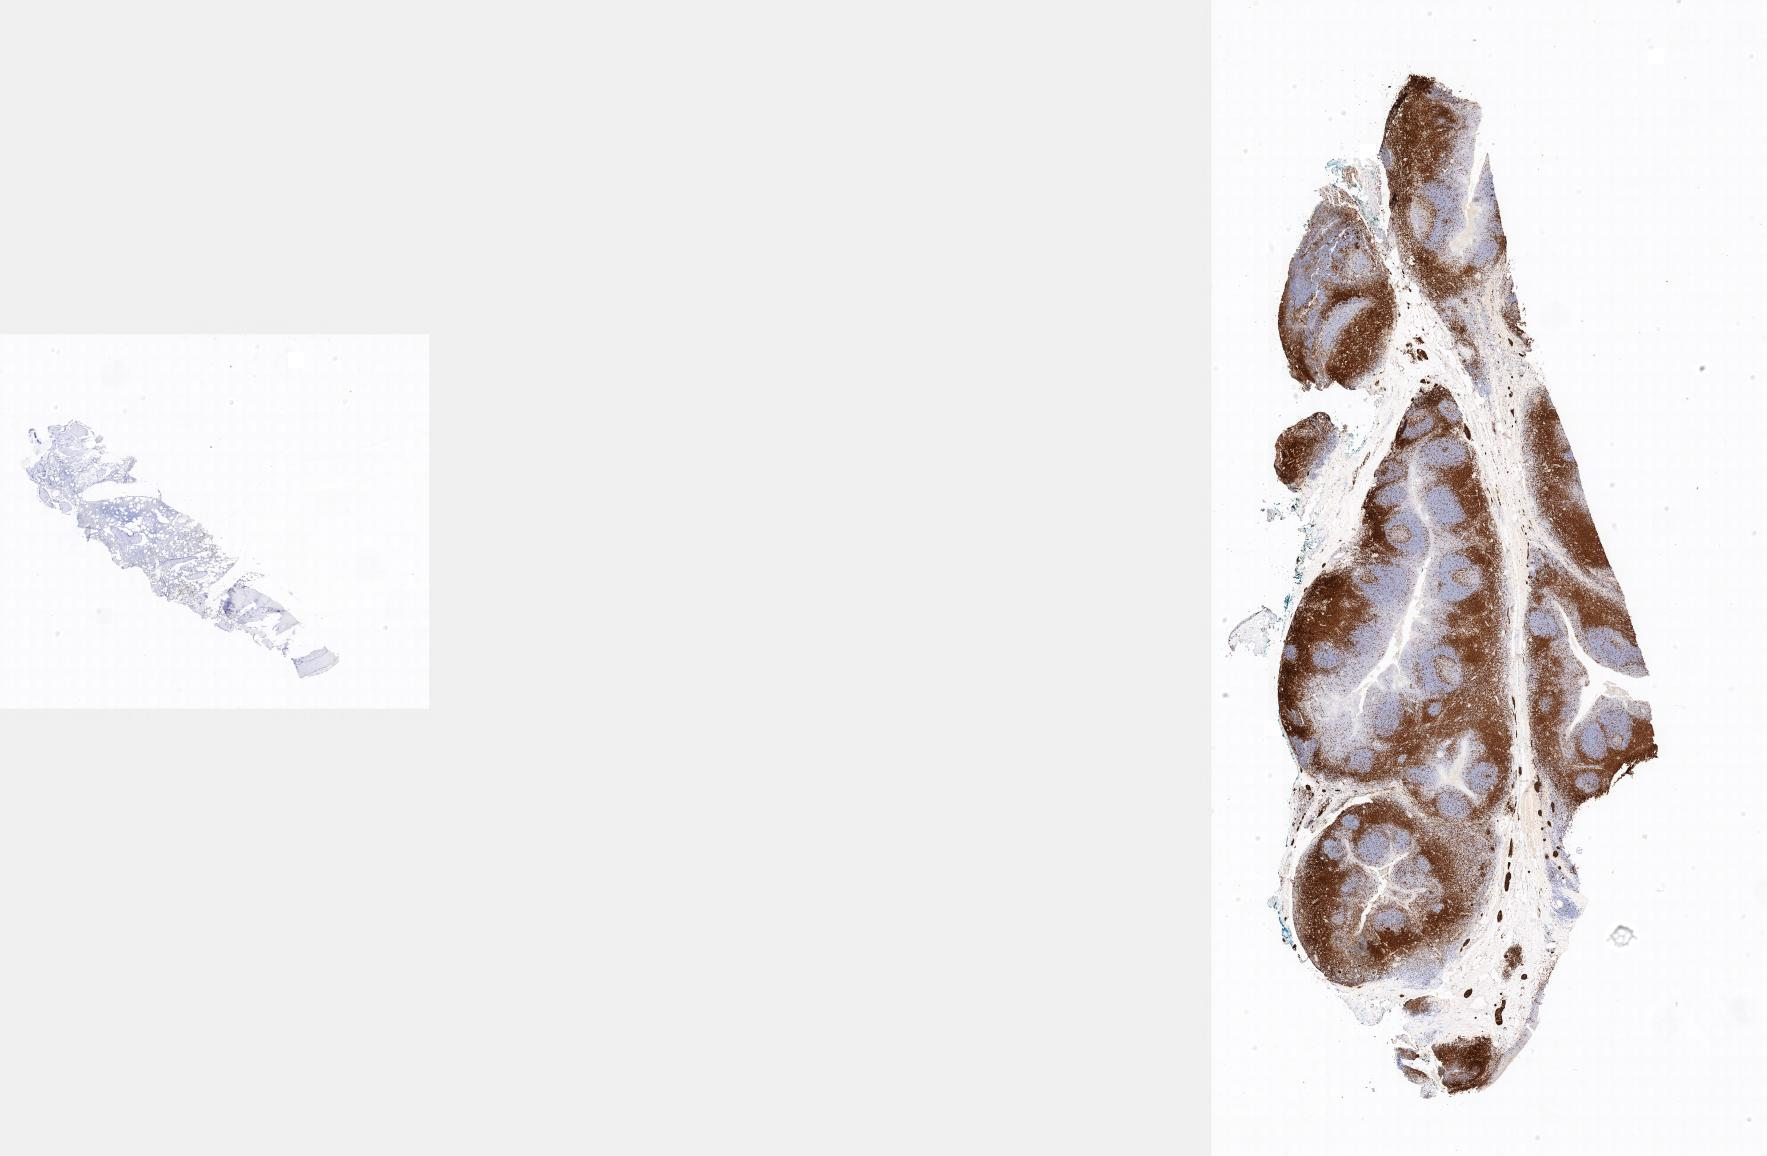
Whole-slide image, immunohistochemical stain for CD3 — shown as a low-resolution overview of the whole scanned area, tumor tissue, anatomic site: bone marrow. Patient: female, age at initial diagnosis 4 years.
- histologic diagnosis: Burkitt lymphoma, NOS